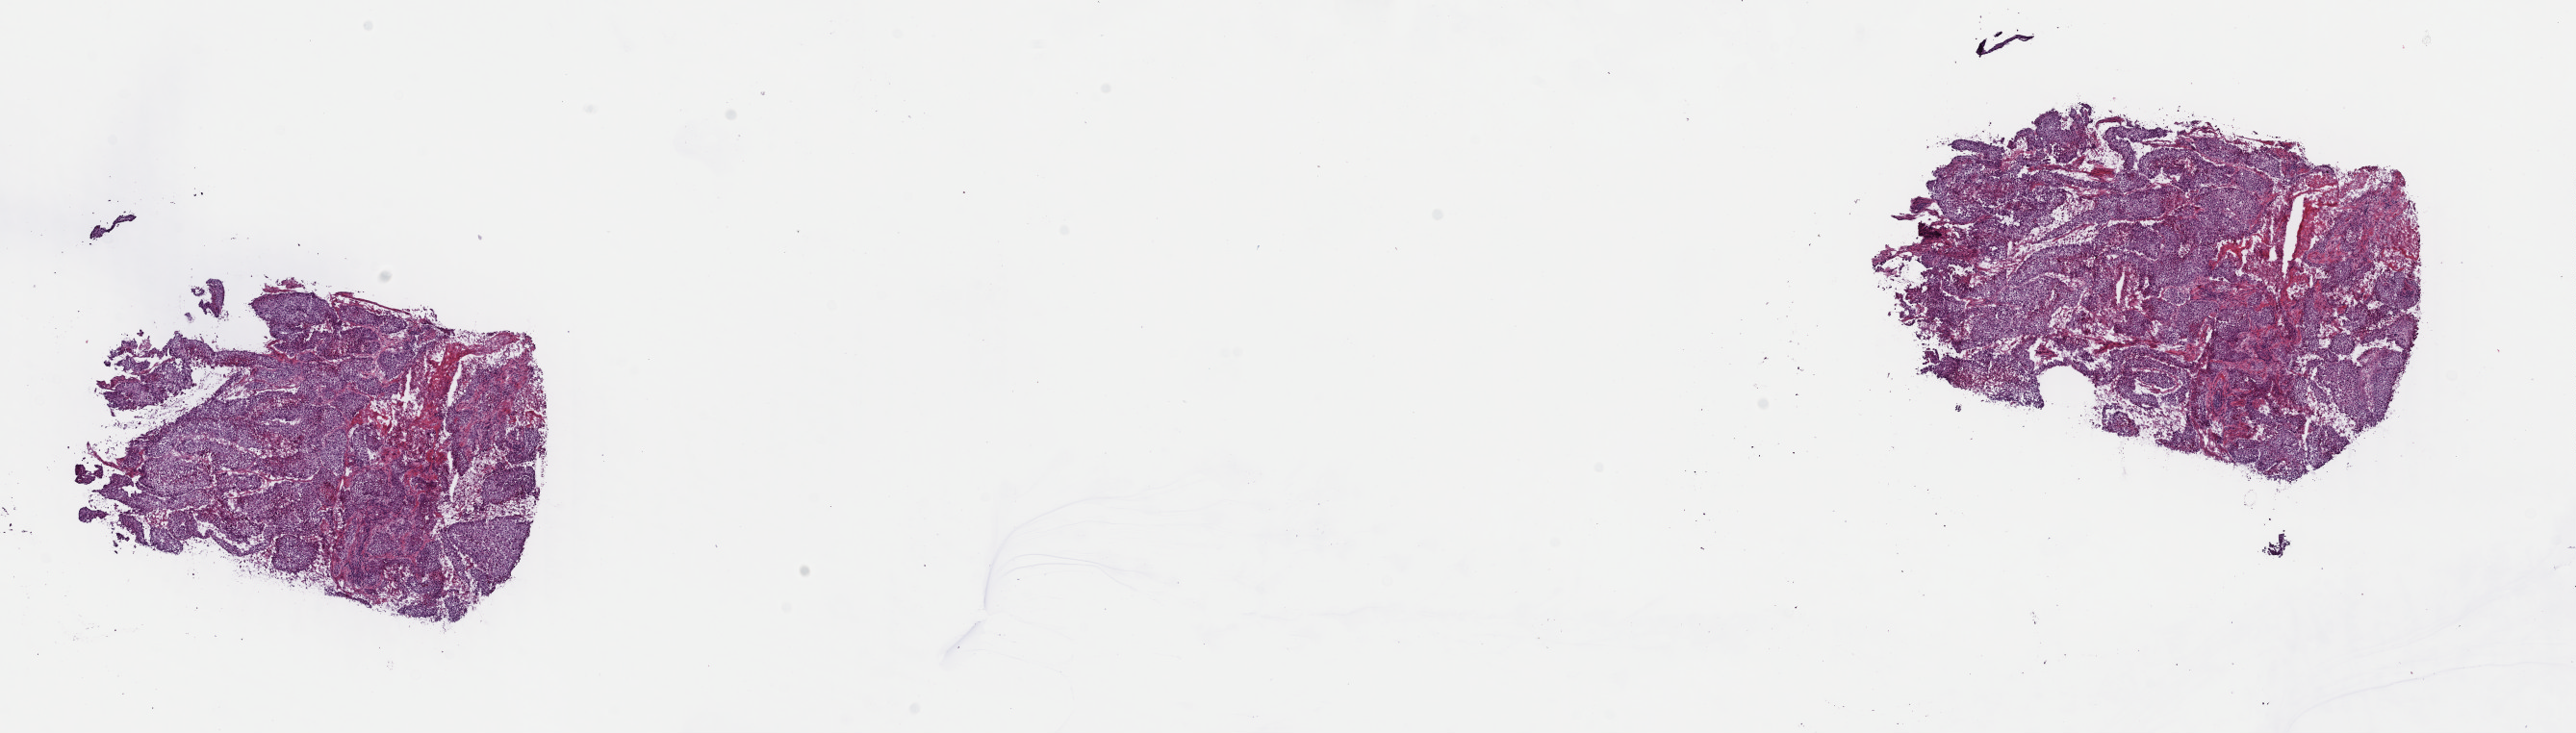
Whole-slide histology image, H&E — low-resolution overview of the scanned area, about 21.1 x 6.0 mm, frozen section from the top of the tissue portion, primary tumour sample from the lung. Male patient; age at initial diagnosis 63 years. Composition of this section per pathologist review: tumour cells 70%, tumour nuclei 70%.
Diagnosis: Squamous cell carcinoma, NOS (lower lobe, lung).